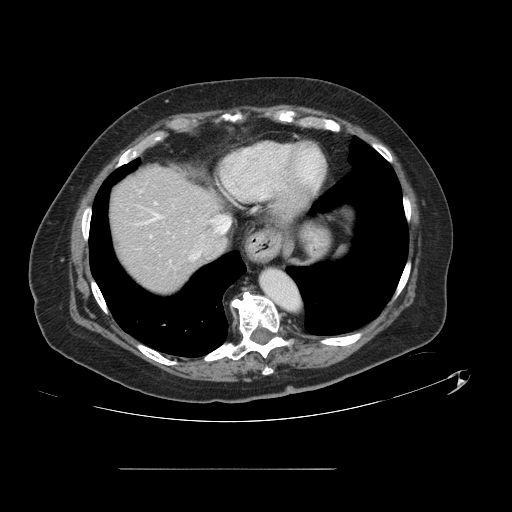
Contrast-enhanced abdominal CT, one axial slice. 120 kVp. Soft-tissue window (W 400 / L 40 HU). 2.5 mm slice thickness. 512 × 512 image matrix. Female patient, age 75 years. Case-level facts recorded for this patient, not image findings: diagnosis: colorectal cancer liver metastases, imaged before liver resection; multiple liver metastases: no; largest metastasis: 2.4 cm; disease in both lobes: no.
Structures marked on this image (expert manual segmentation):
- hepatic veins: box from (x=153, y=214) to (x=231, y=260) px
- liver: (x=109, y=167)–(x=219, y=293)
- planned liver remnant (the part of the liver to remain after resection): (x=109, y=167)–(x=220, y=292)